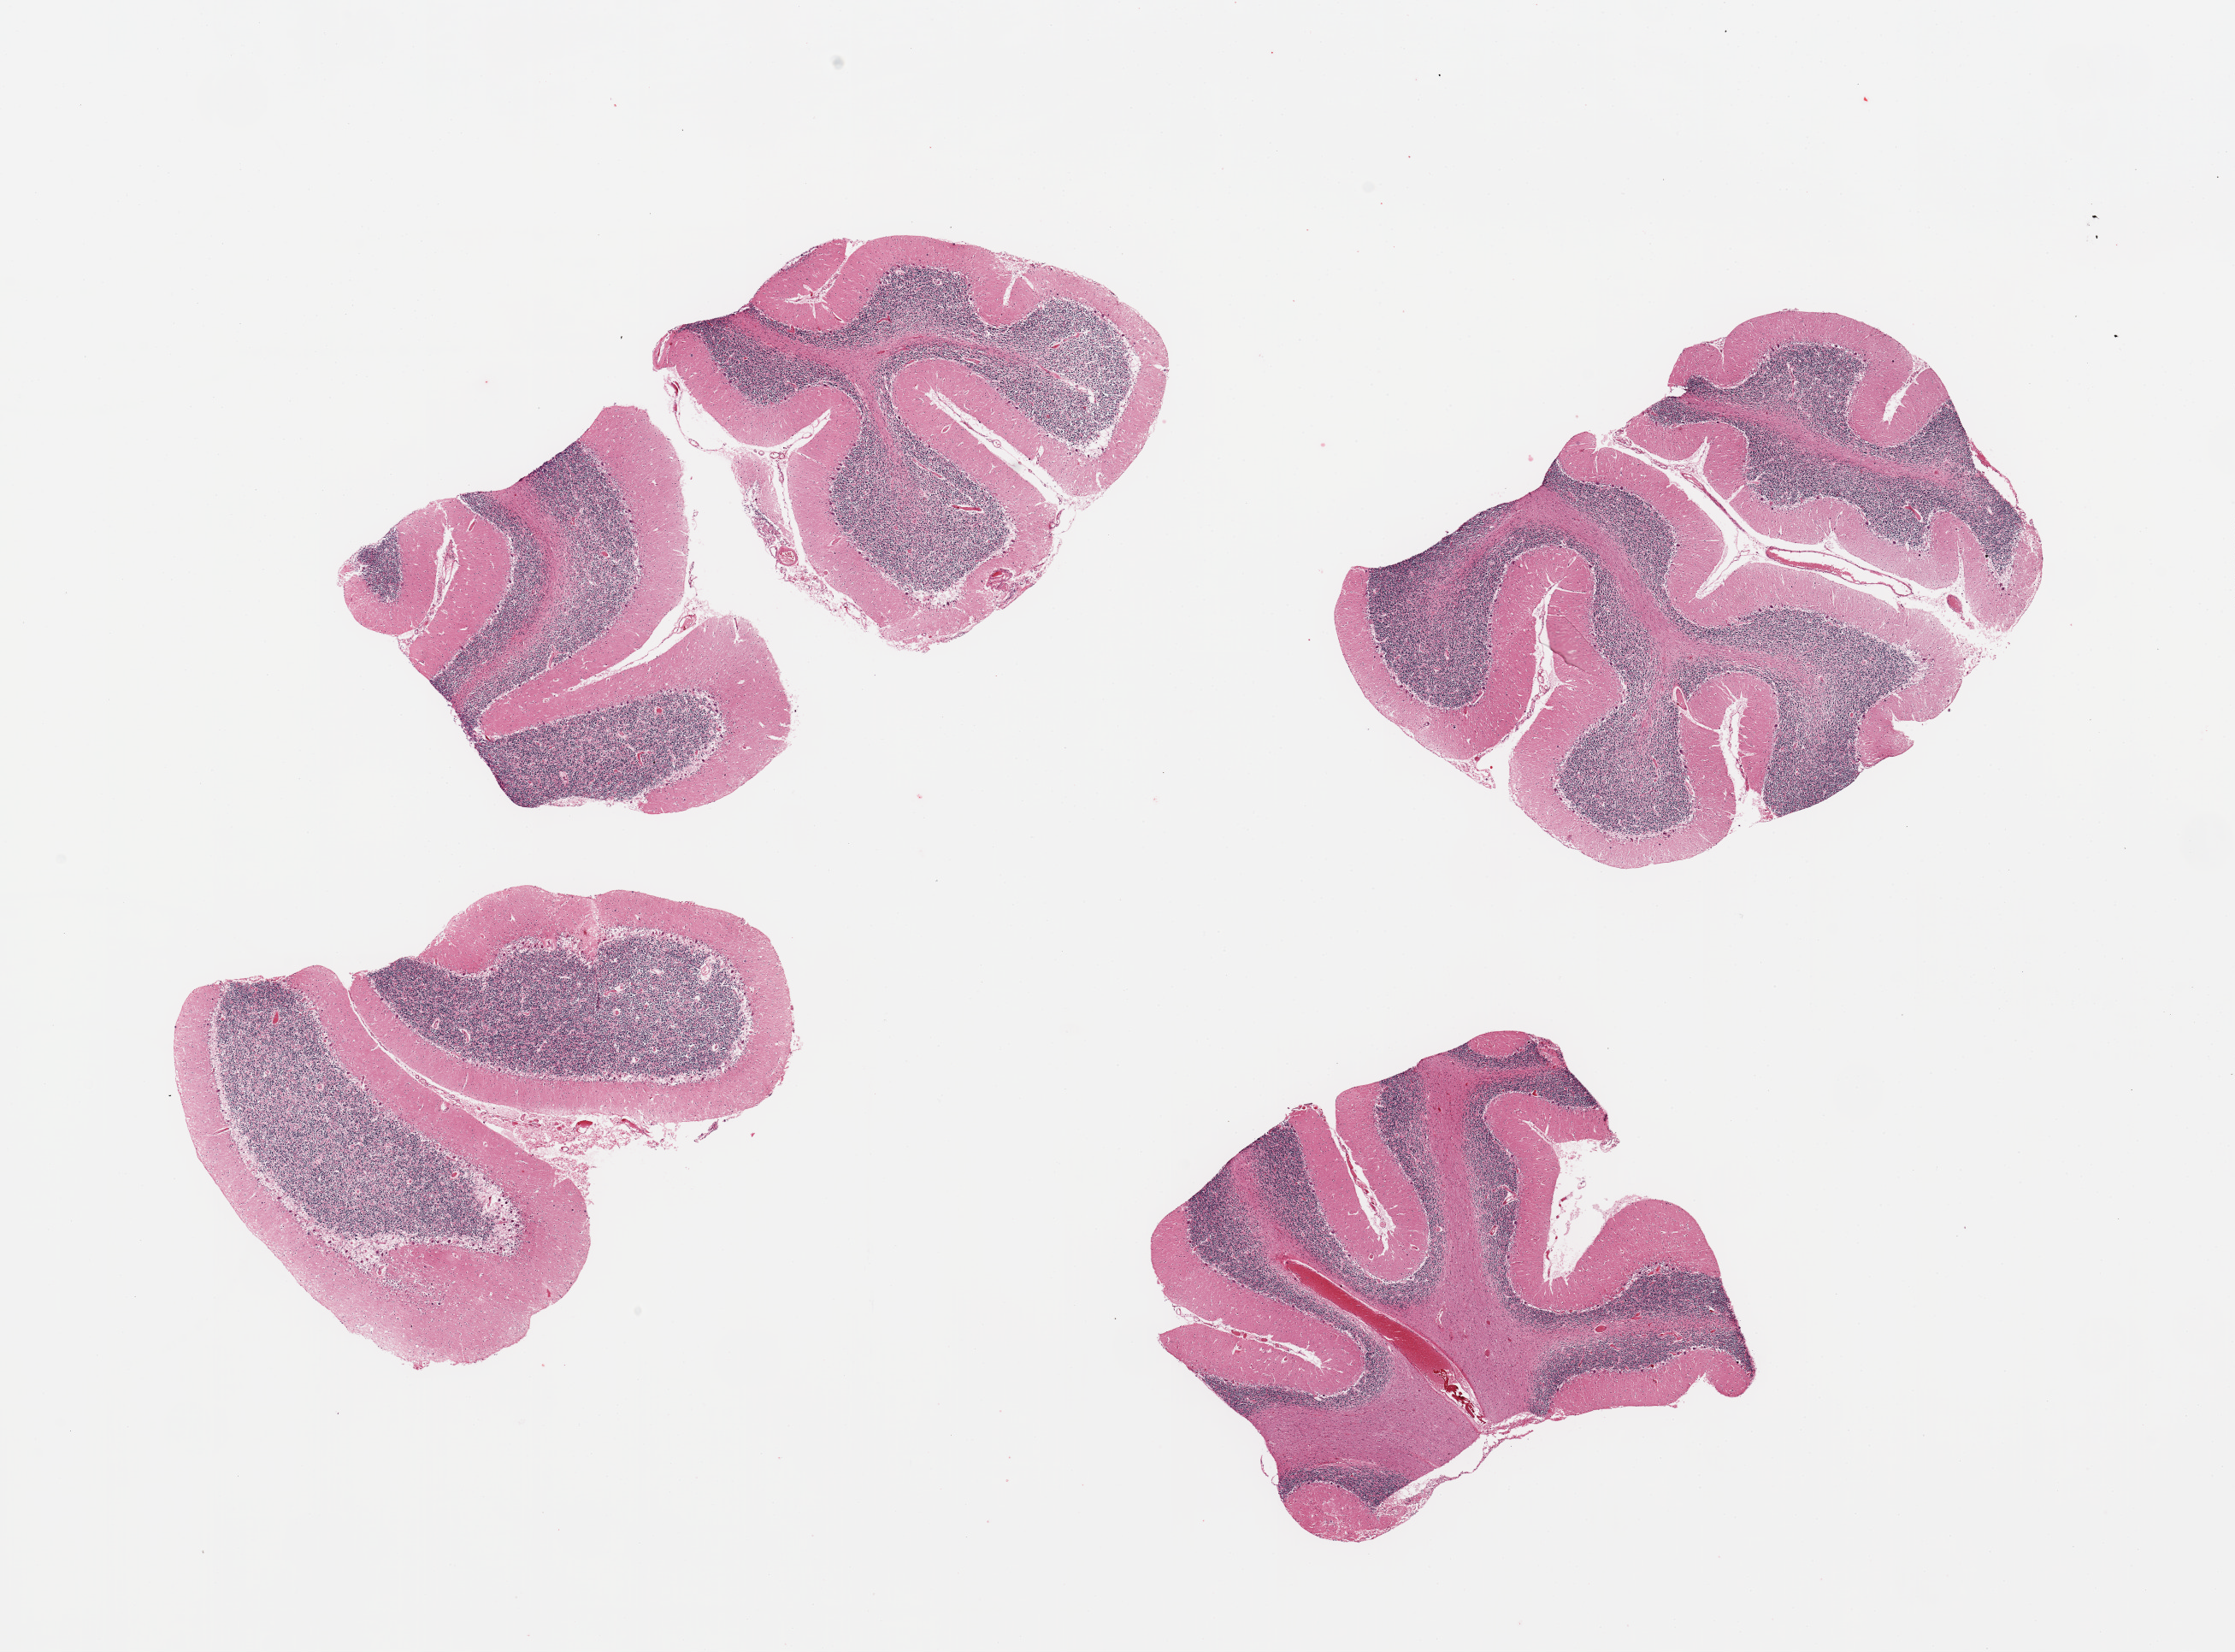
Haematoxylin and eosin whole-slide image — whole scanned area (about 20.7 x 15.3 mm) shown as a low-resolution overview. PAXgene-fixed, paraffin-embedded tissue. Section of cerebellum (target tissue). Donor tissue sample. Donor: female.
Review note (as recorded): 4 pieces, no abnormalities.